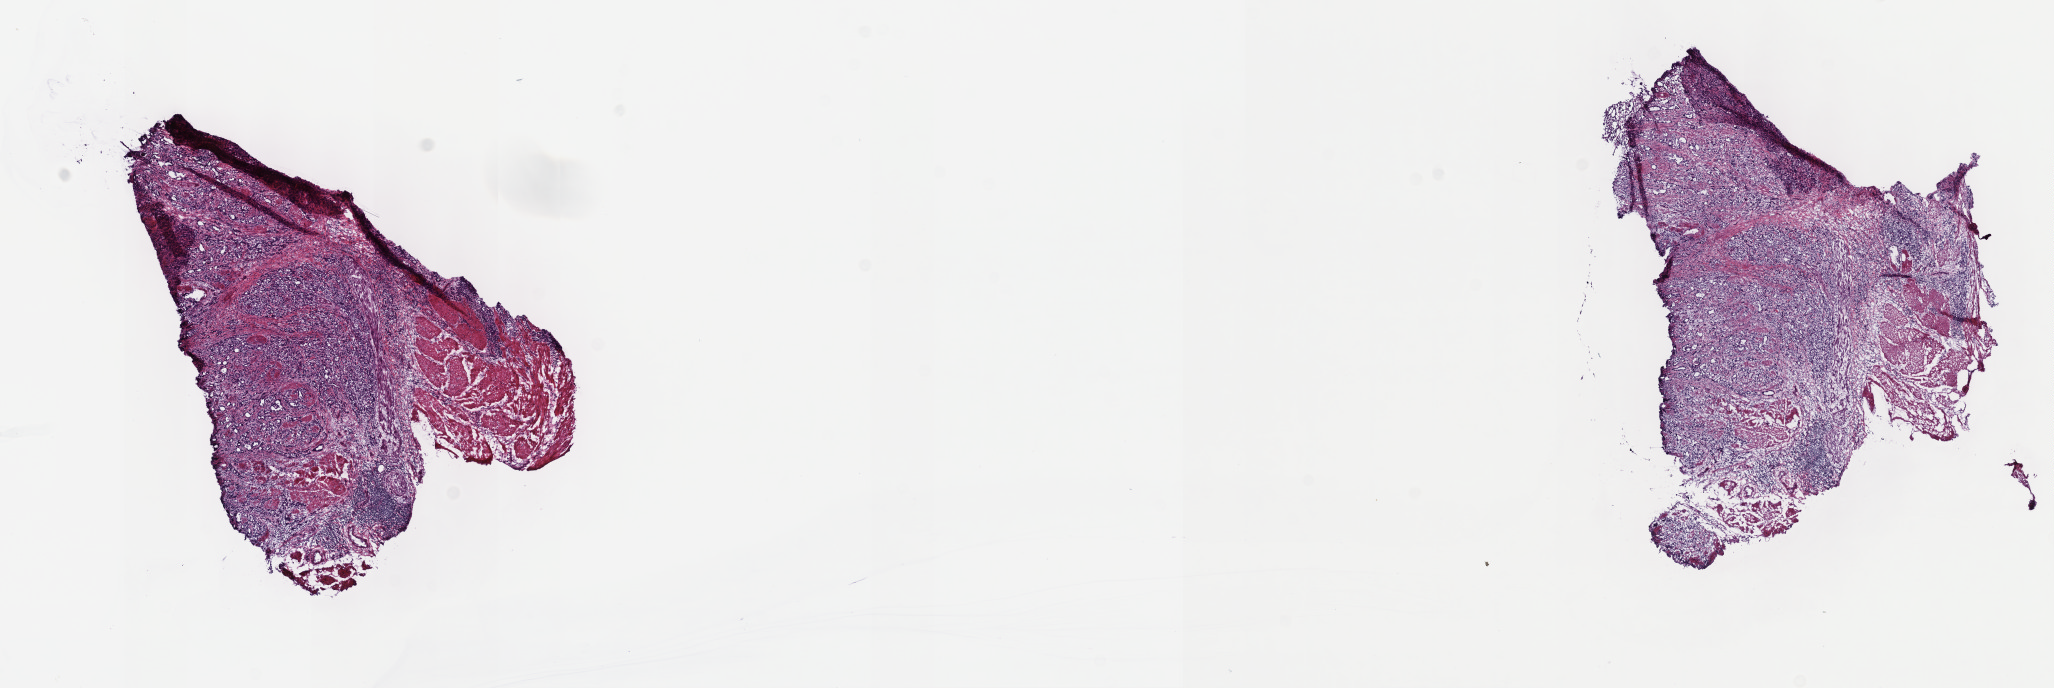
Digitized H&E-stained tissue section (whole slide), whole scanned area (about 16.6 x 5.6 mm) shown as a low-resolution overview. Frozen section from the top of the tissue portion. Sample: primary tumour, esophagus. Patient: male, age at initial diagnosis 61 years. Histologic grade: G3 (poorly differentiated). Composition of this section per pathologist review: tumour cells 70%, tumour nuclei 70%, normal cells 0%, stromal cells 30%, necrosis 0%. Infiltration values recorded for this section: lymphocyte infiltration 40%, monocyte infiltration 20%, neutrophil infiltration 20%.
- diagnosis: Adenocarcinoma, NOS (lower third of esophagus)
- AJCC pathologic stage: IIIA (7th edition)
- lymph nodes positive (case pathology): 1 of 43 examined